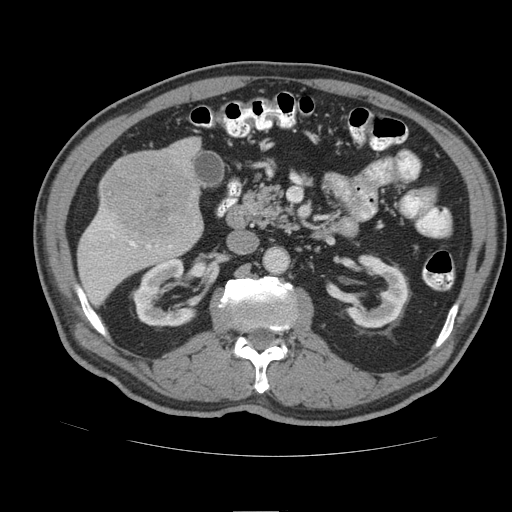
Contrast-enhanced abdominal CT (liver protocol), one axial slice. Slice 35 of 105 in the series (ordered by position). Soft-tissue window (W 400 / L 40 HU). 2.5 mm slice thickness. 512 × 512 image matrix, field of view 380 × 380 mm. From the clinical record (not read from this slice): diagnosis: hepatocellular carcinoma (patient treated with transarterial chemoembolisation; whether this scan precedes or follows treatment is not stated here); TNM stage (as recorded): Stage-IIIB; Child-Pugh class: A.
Structures marked on this image (semi-automatically segmented with operator editing):
- liver parenchyma outside the tumour (the mass and vessels are separate outlines, so this box may not span the whole liver): bounding box <78,137,202,304> (left, top, right, bottom; pixels)
- mass: <102,153,198,241>
- liver vessels: <107,224,171,248>